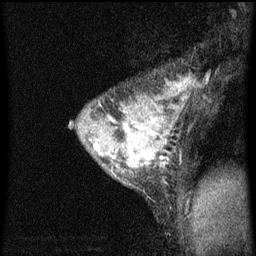
Breast MRI (dynamic contrast-enhanced), one sagittal slice. Slice 48 of 60 in the series (ordered by position). Dynamic contrast-enhanced series, image 2 of 3 at this slice position (ordered by acquisition). 1.5 T. TE 4.2 ms, TR 8 ms. 2 mm slice thickness. 256 × 256 image matrix, field of view 180 × 180 mm. Female patient, age 33 years.
Outlined on this slice (semi-automatic segmentation, software-assisted and operator-edited):
- analysis volume of interest (the breast-tissue region the enhancement analysis was run in; not a lesion): bounding box (x1, y1, x2, y2) in pixels: (70, 68, 195, 215)
- tumour enhancement mask (voxels above the 70 % enhancement threshold inside the analysis volume of interest): (95, 104, 169, 175)